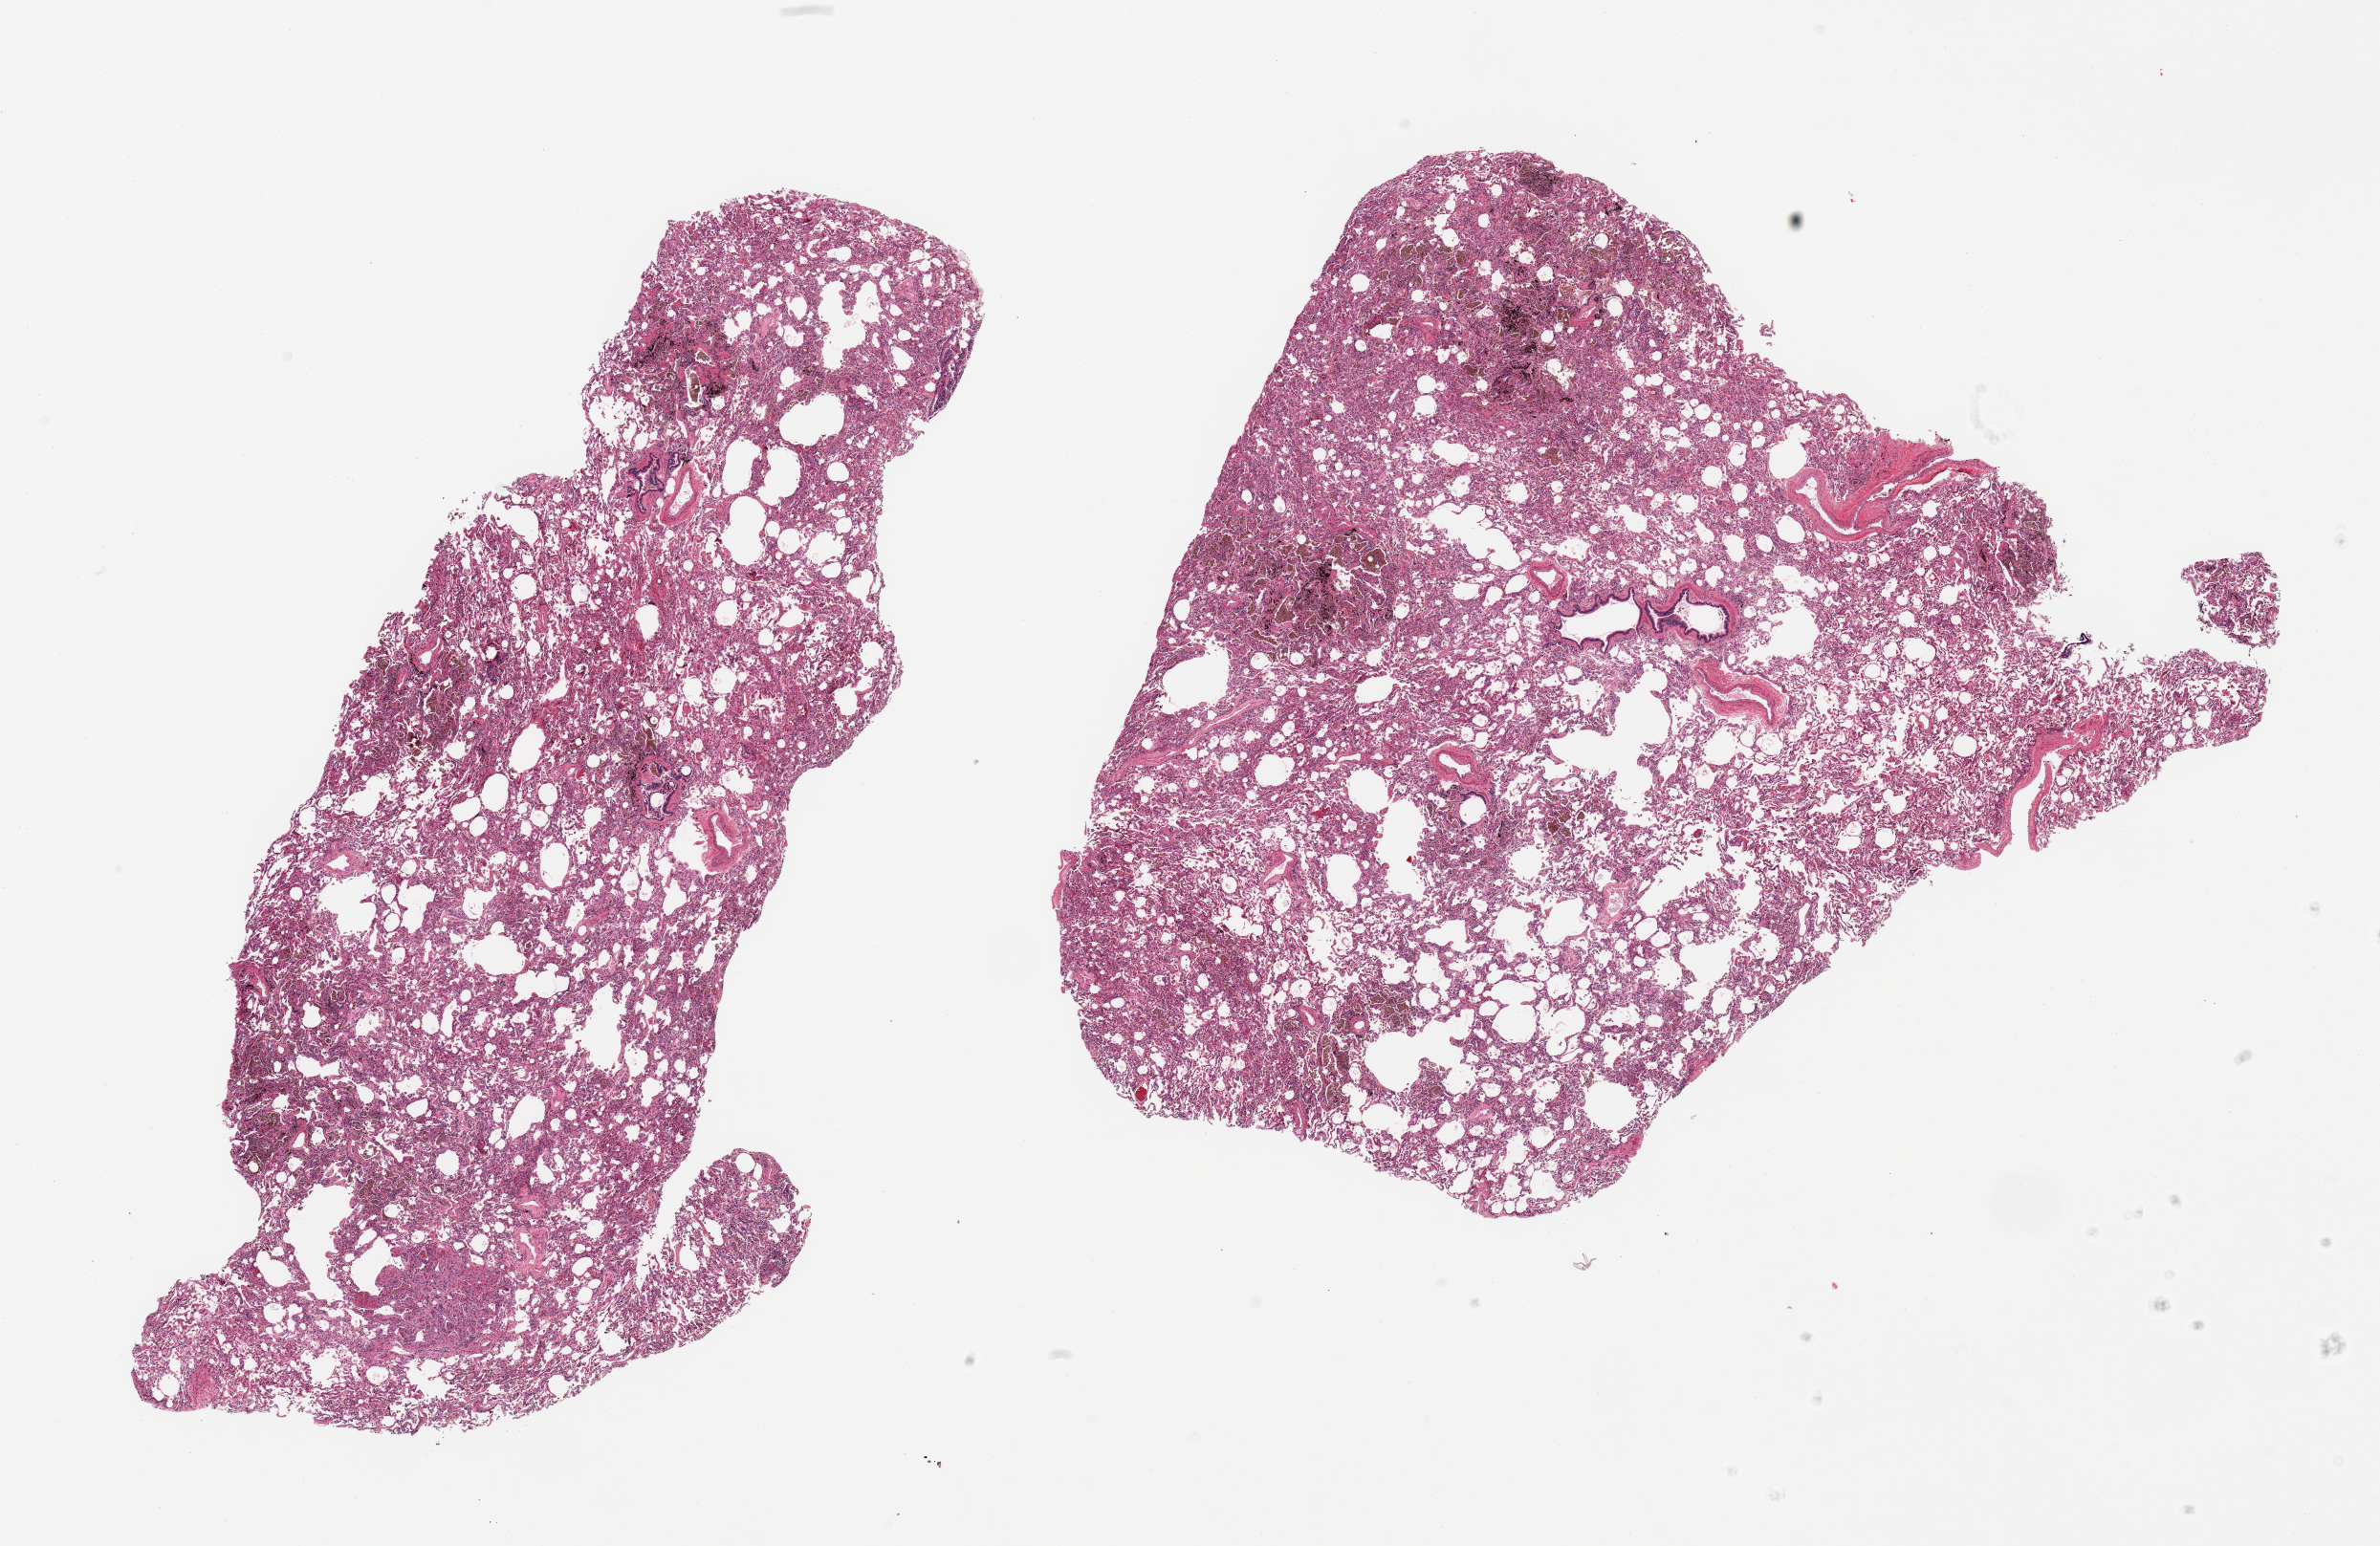
Haematoxylin and eosin whole-slide image, brightfield — whole scanned area (about 19.7 x 12.8 mm, from a 20x scan) shown as a low-resolution overview; PAXgene-fixed, paraffin-embedded tissue; section of lung (target tissue); tissue donor sample. Donor sex: female.
- pathologist's review note for this sample: 2 pieces; some atelectasis, numerous intra-alveolar pigmented macrophages